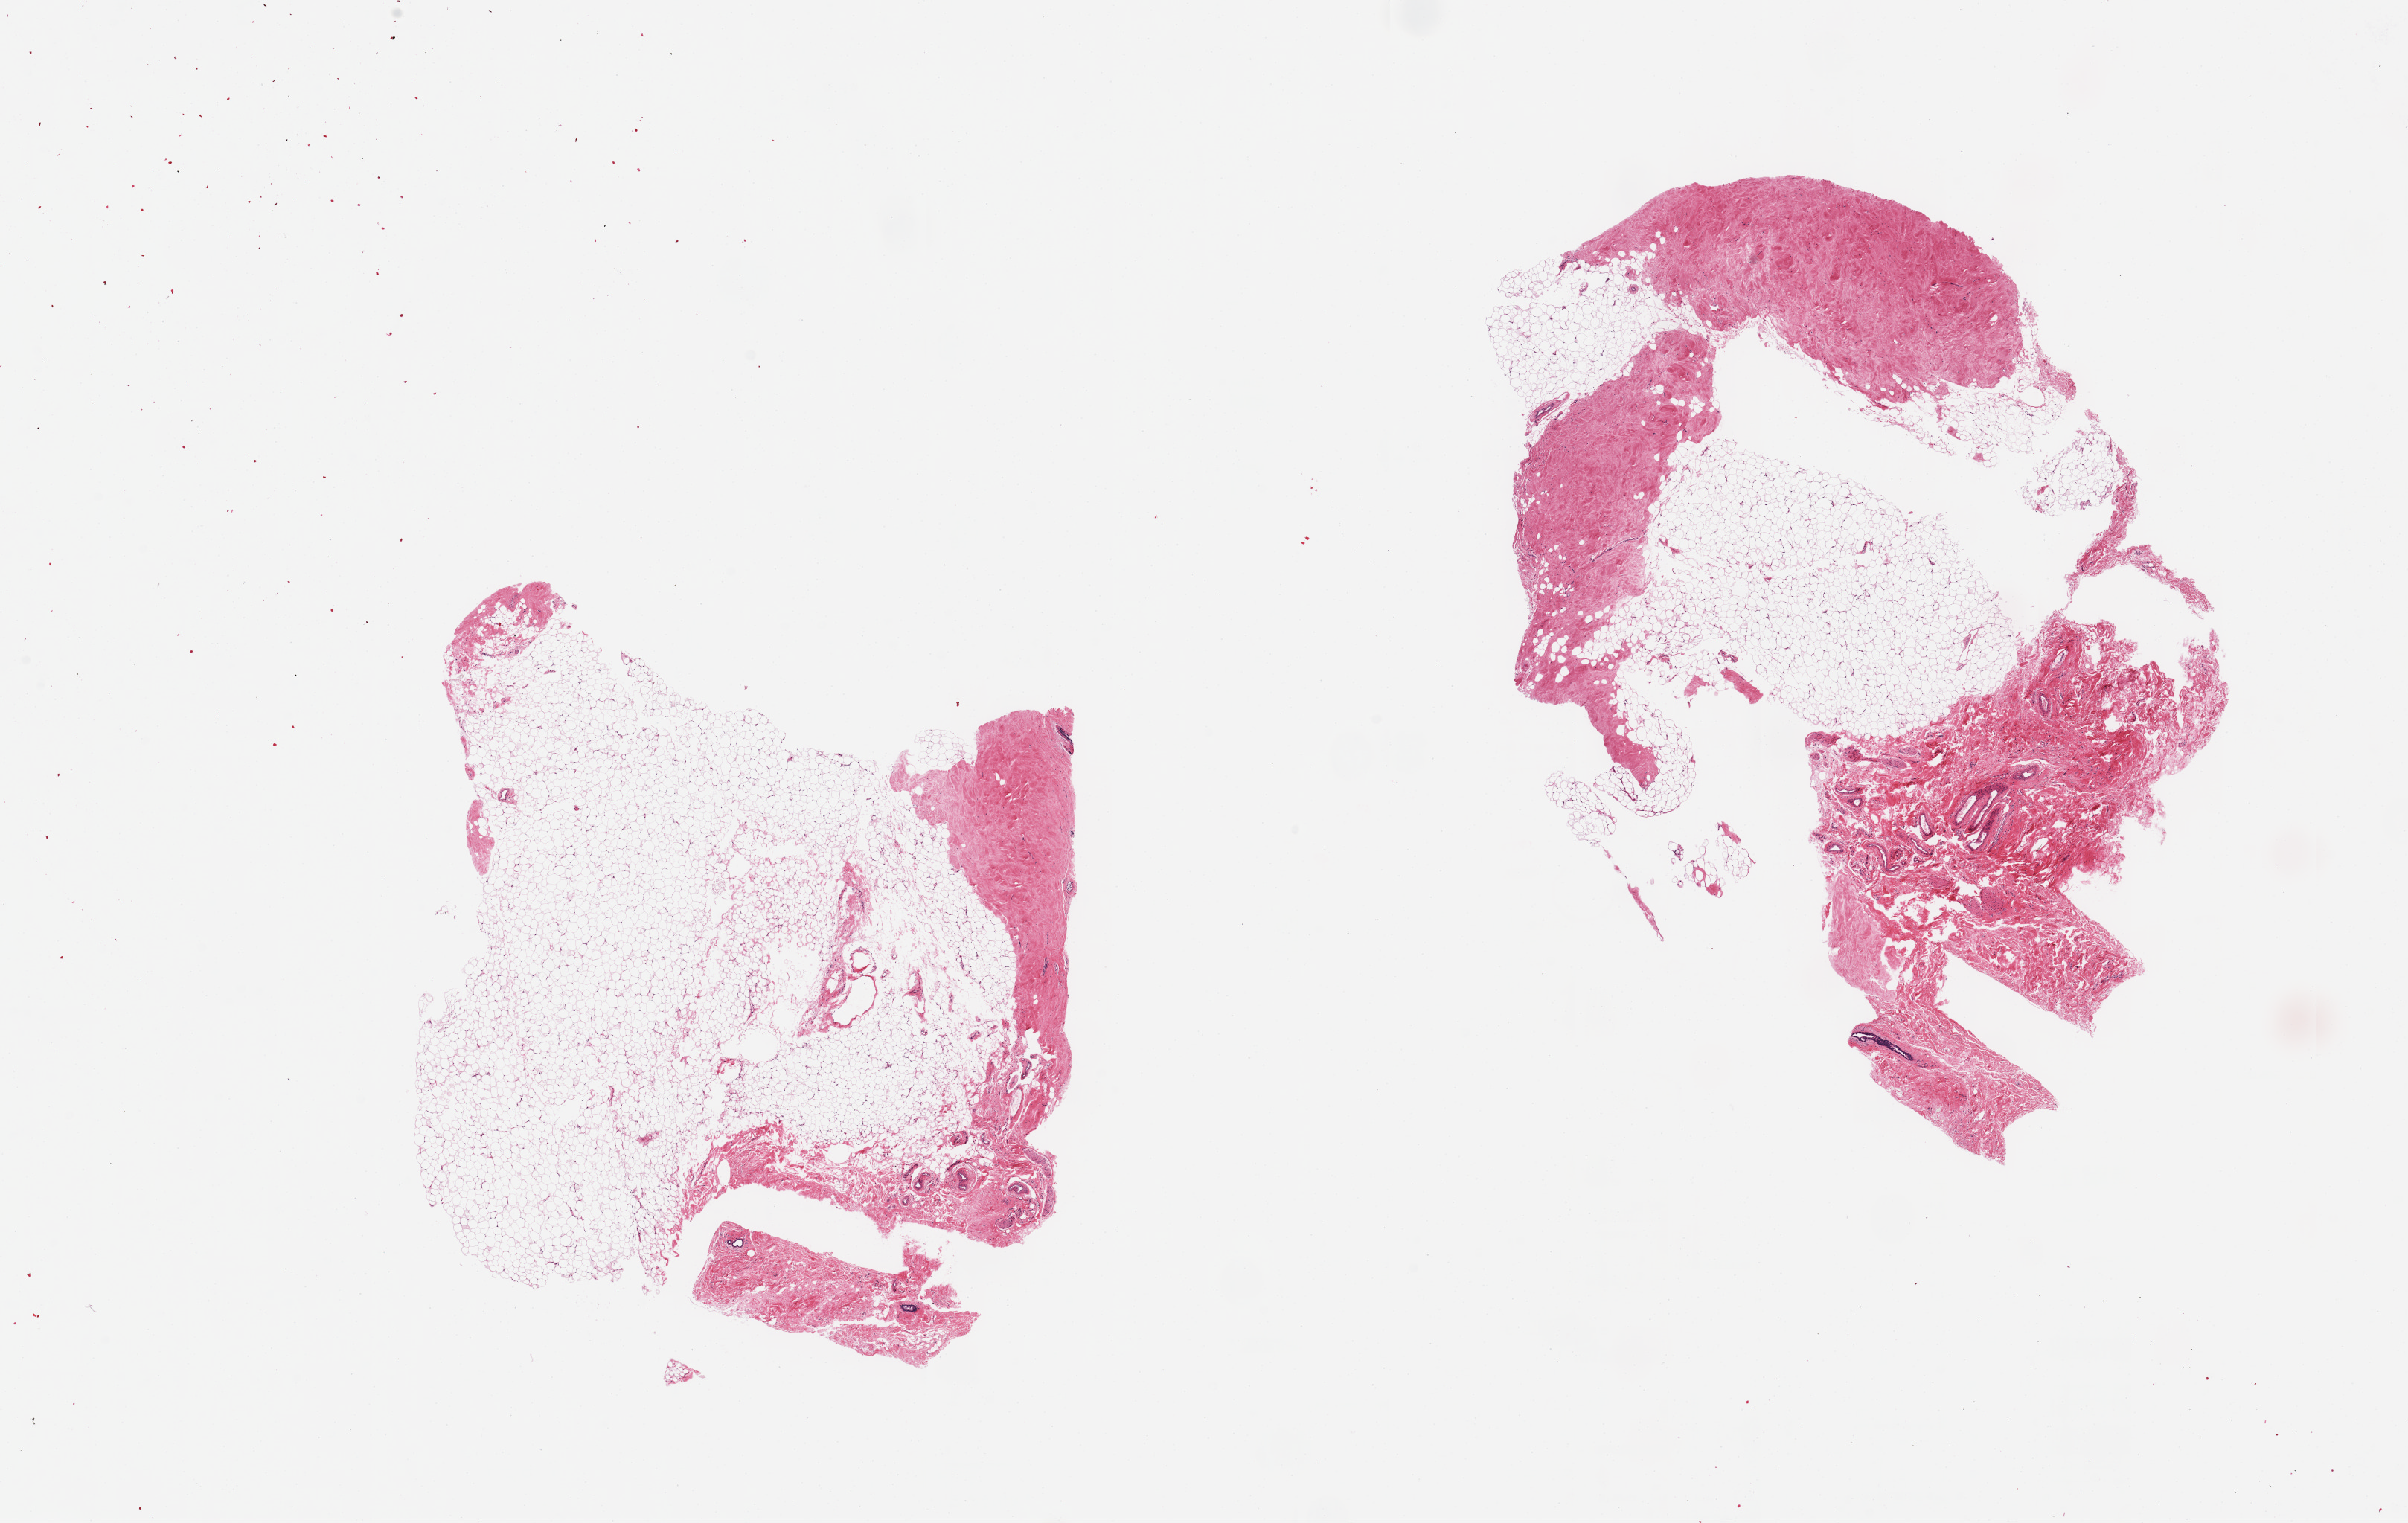
Hematoxylin and eosin (H&E) whole-slide image — a low-resolution overview of the entire scanned area, about 25.6 x 16.2 mm. PAXgene-fixed paraffin-embedded (PFPE) section. Section of breast (target tissue). Donor tissue sample. Donor: female.
• reviewer comment on this tissue sample: 2 pieces; 80% and 50% adipose tissue and dense fibrovascular tissue with single ducts